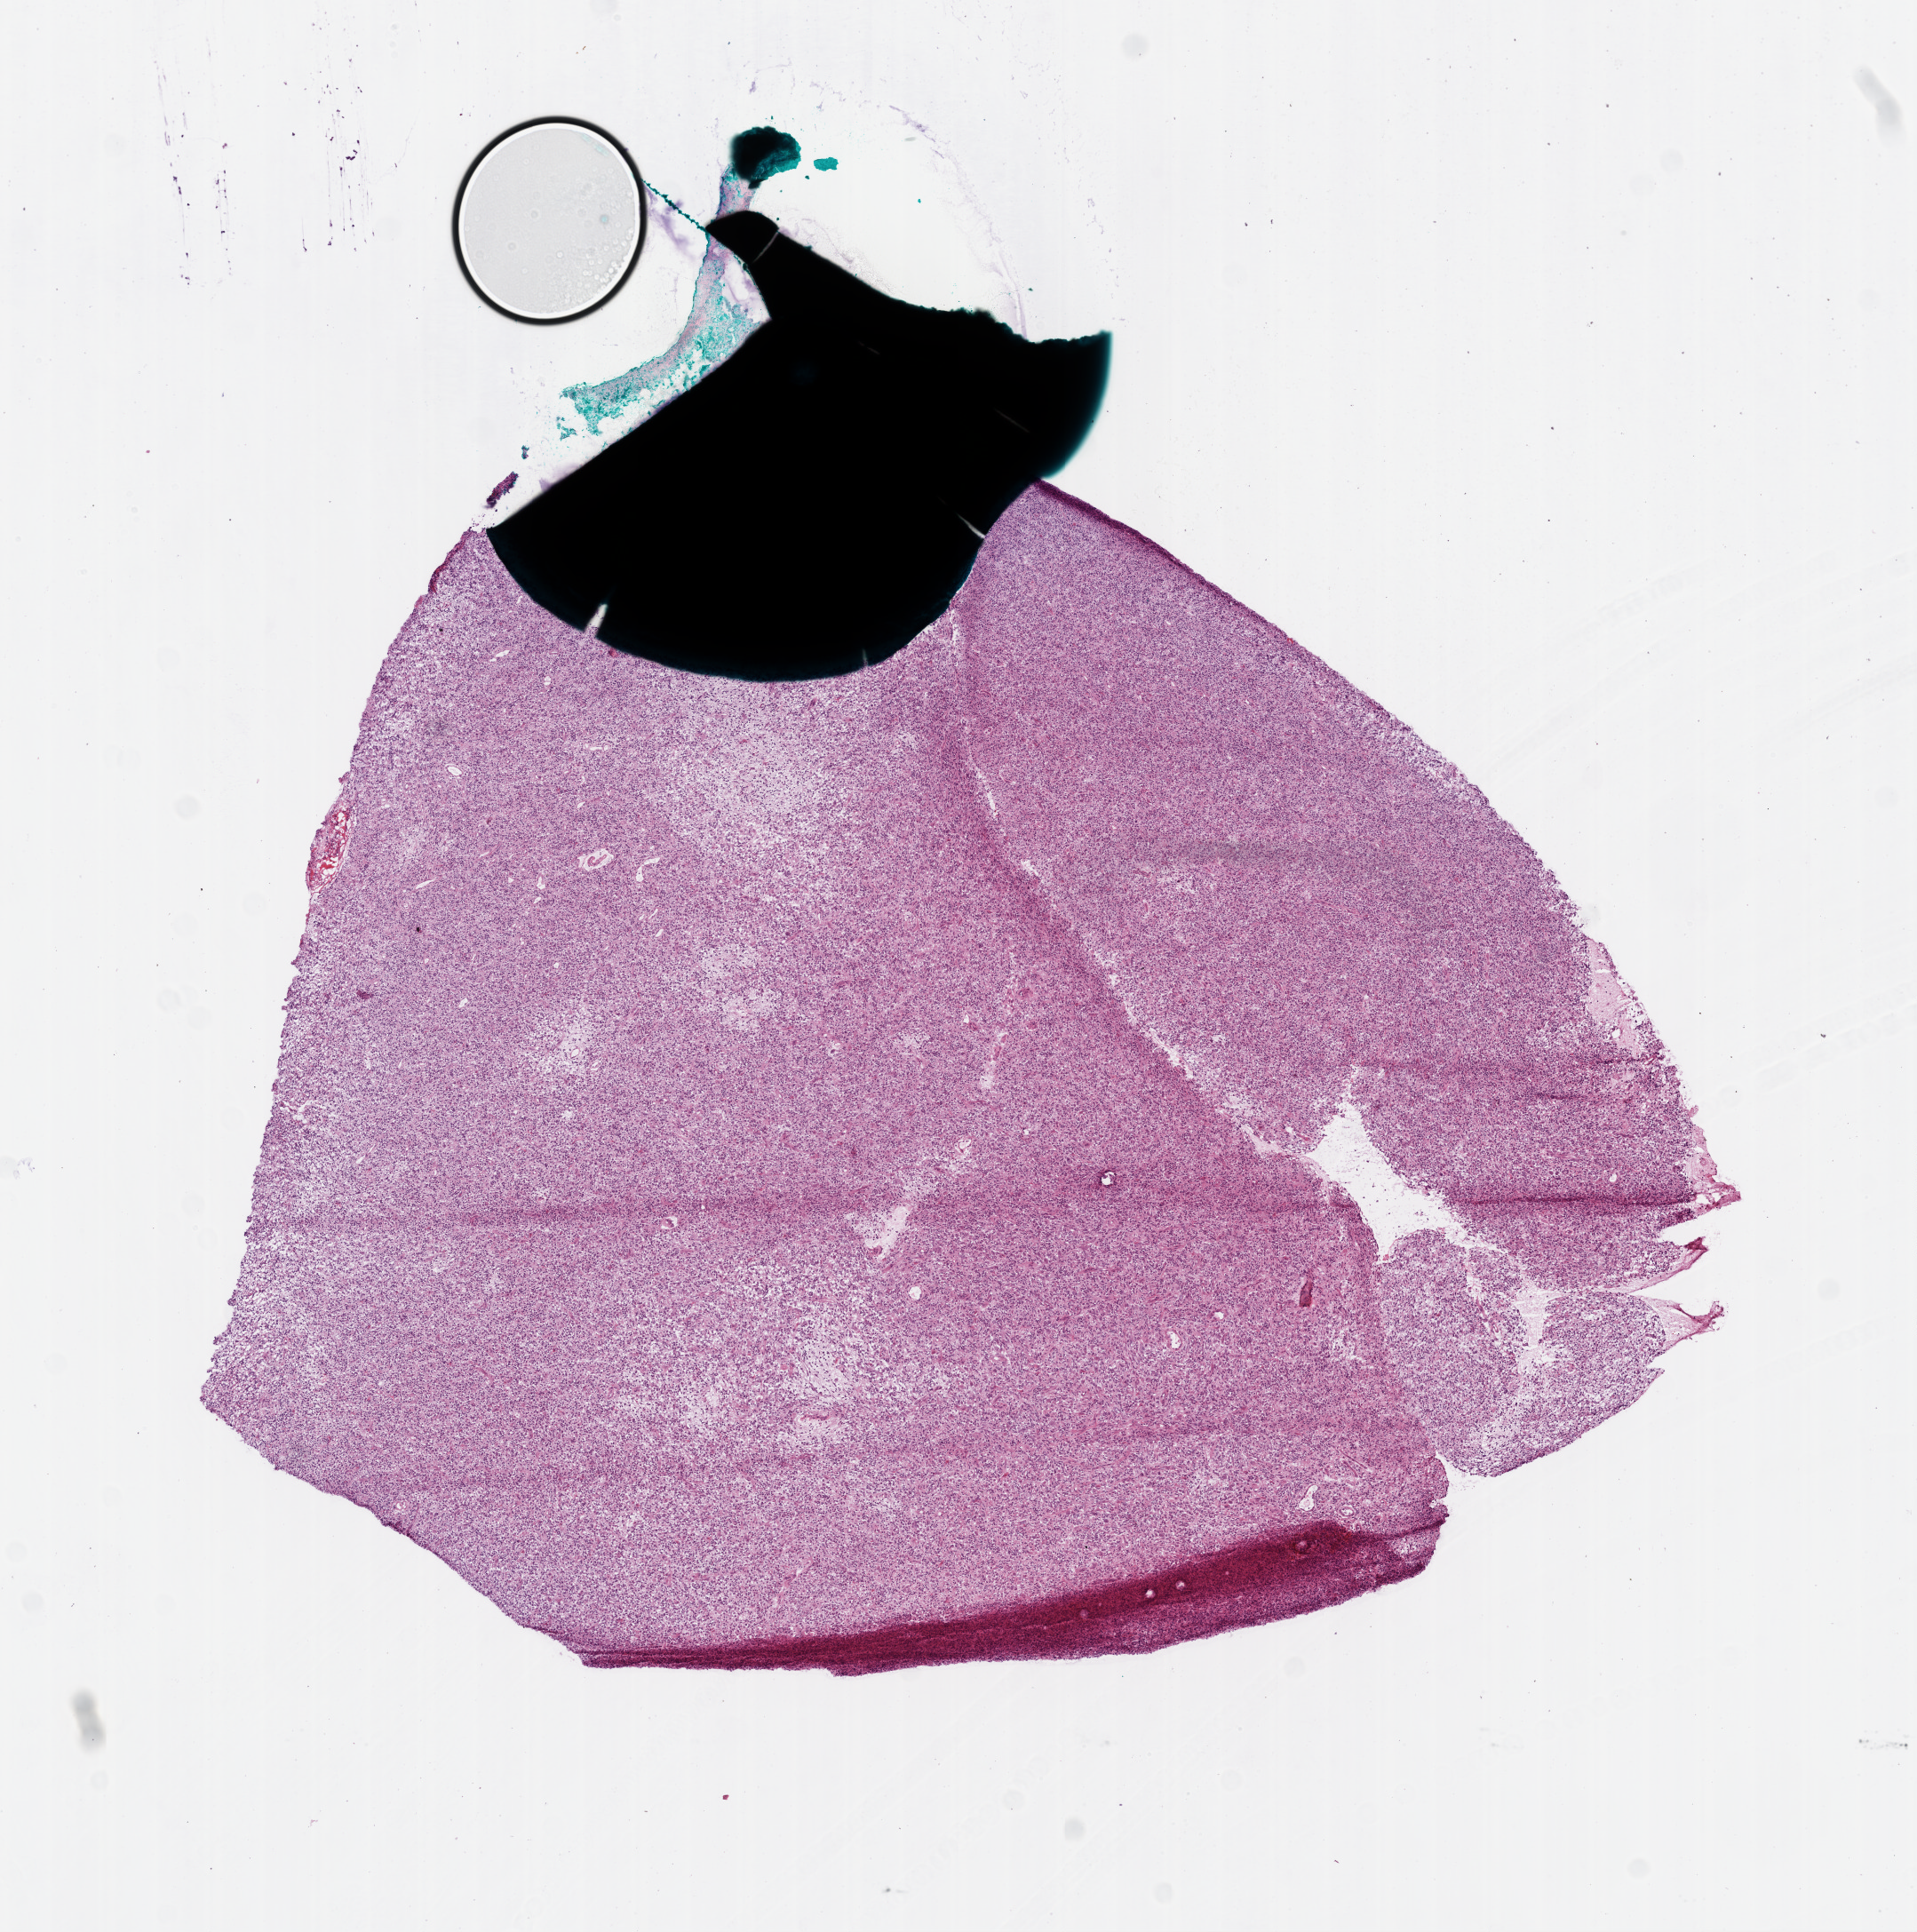
Hematoxylin and eosin (H&E) stained whole-slide image, a low-resolution overview of the entire scanned area, about 8.7 x 8.8 mm (slide scanned at 20x). Frozen section. Brain, primary tumour sample. Male, age 53 years at initial diagnosis.
Histologic diagnosis: Glioblastoma.